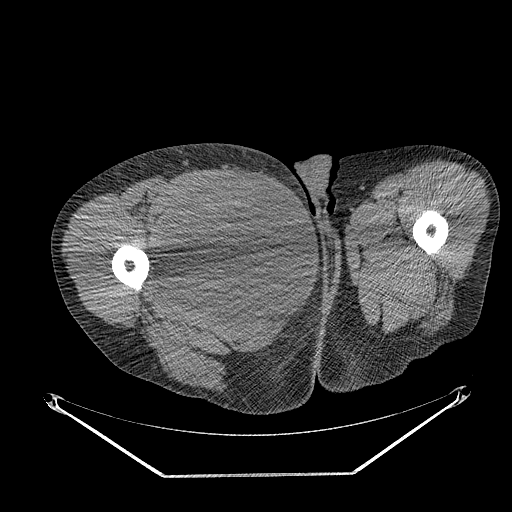
CT of an extremity soft-tissue mass (from a PET/CT study), one axial slice. Position 271 of 311 along the scan axis. Reconstruction kernel STANDARD. 140 kVp. Soft-tissue window (W 400 / L 40 HU). 3.75 mm slice thickness. 512 × 512 image matrix. Male patient. Case-level facts recorded for this patient, not image findings: histological type: undifferentiated - pleiomorphic; grade: high; site of the primary tumour: right thigh.
Outlined on this slice (expert contour drawn on MRI and transferred to this co-registered scan by the dataset authors):
- gross tumour volume including surrounding oedema: bounding box <158,173,268,279> (left, top, right, bottom; pixels)
- gross tumour volume (mass): <158,173,268,279>